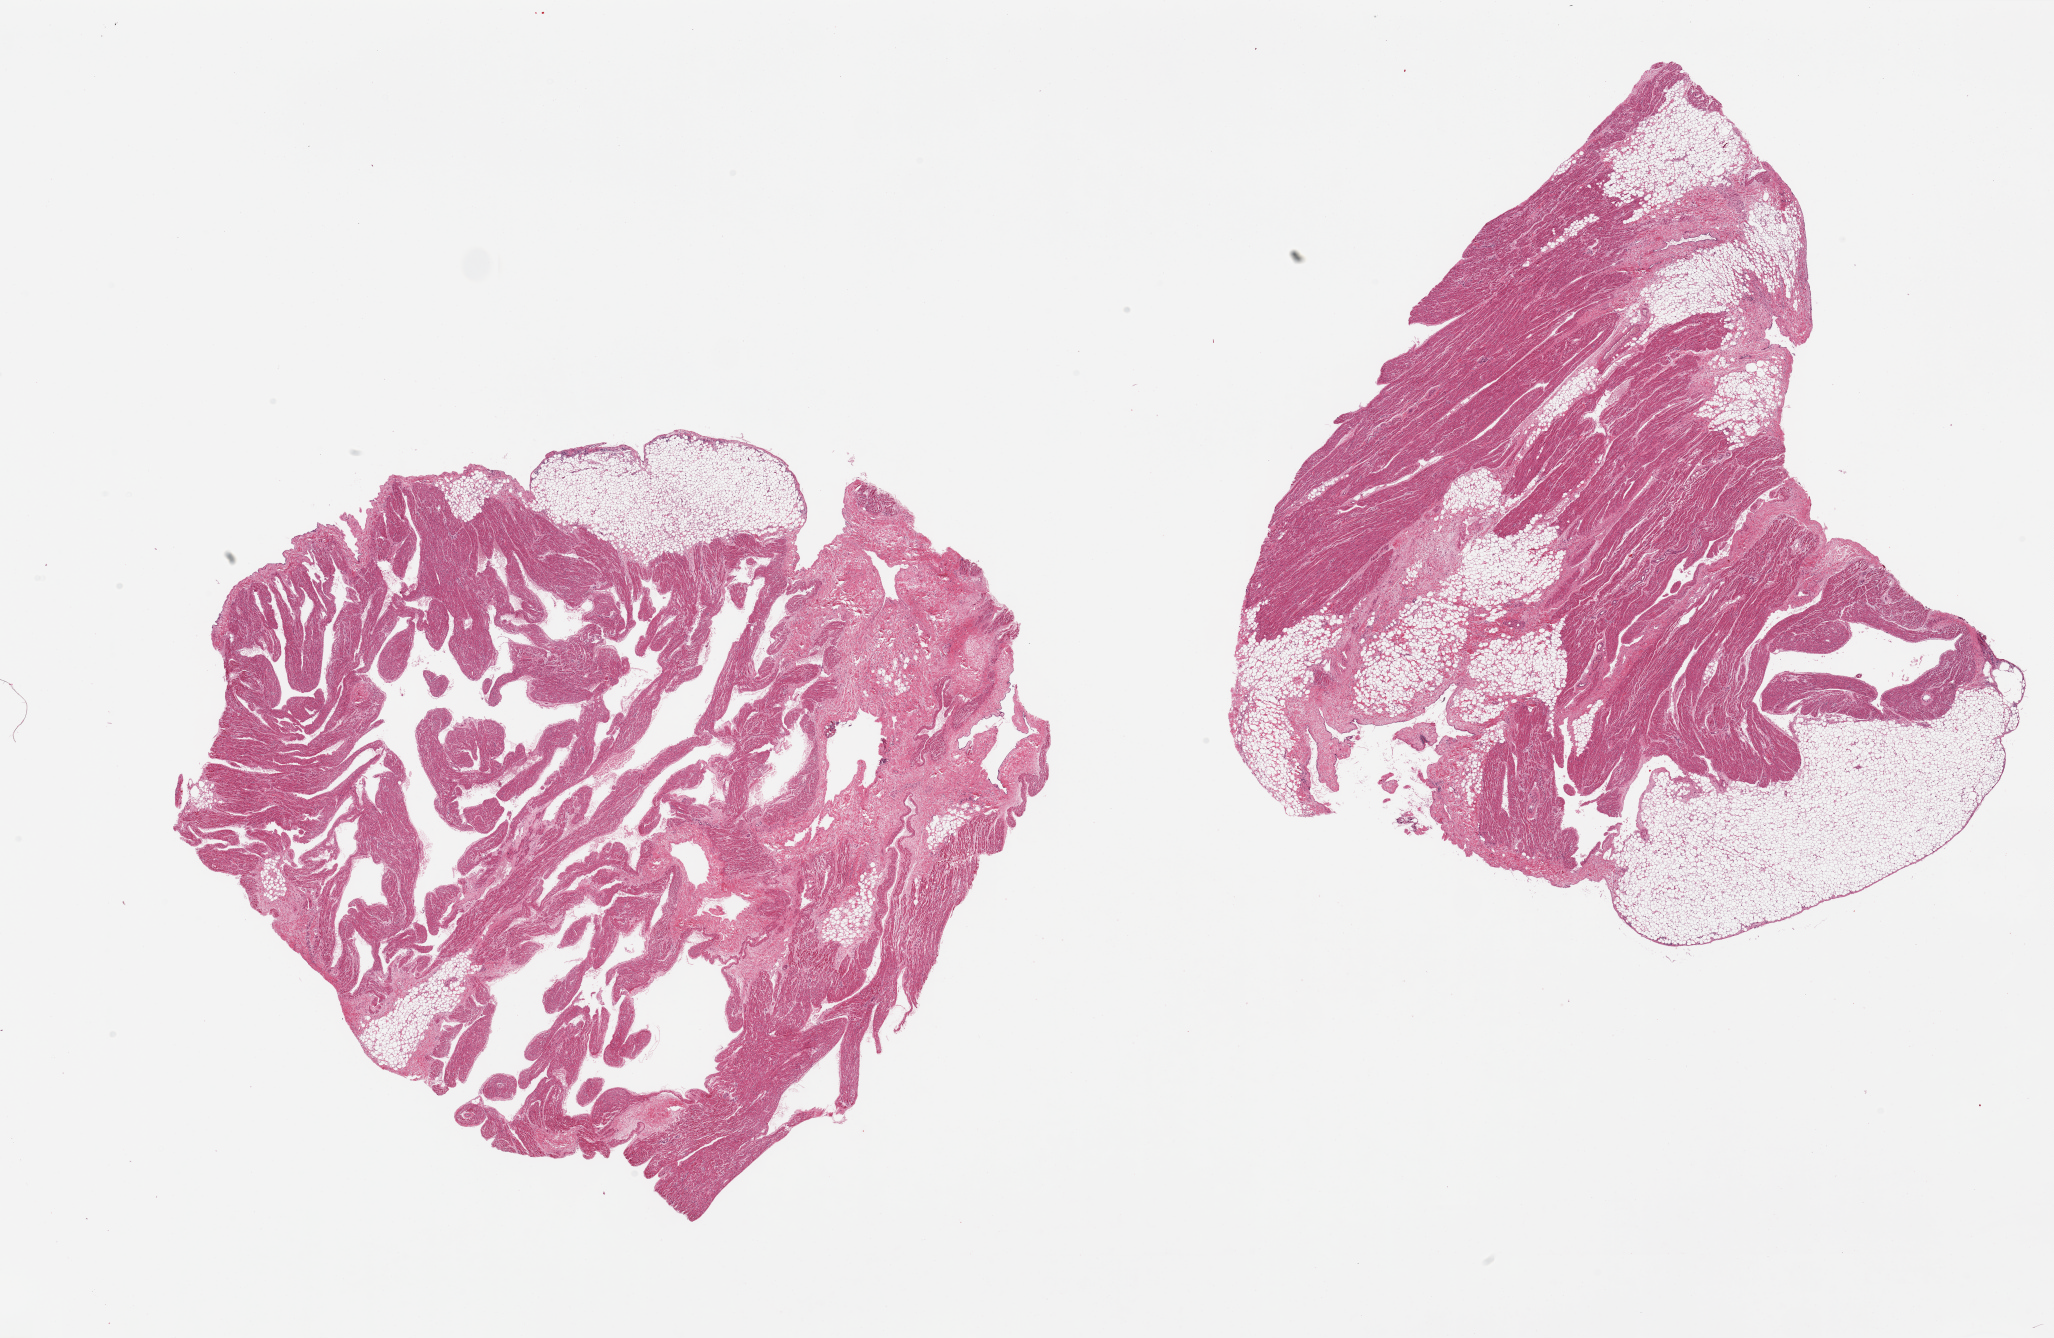
H&E whole-slide image, low-resolution overview of the scanned area, about 32.5 x 21.2 mm. PAXgene-fixed, paraffin-embedded tissue. Target tissue: auricular appendage. Donor tissue sample. Female donor.
Reviewer comment on this tissue sample: 2 pieces; 1 with 50% external and internal fat, other with 20% fibroadipose tissue, internal and external.